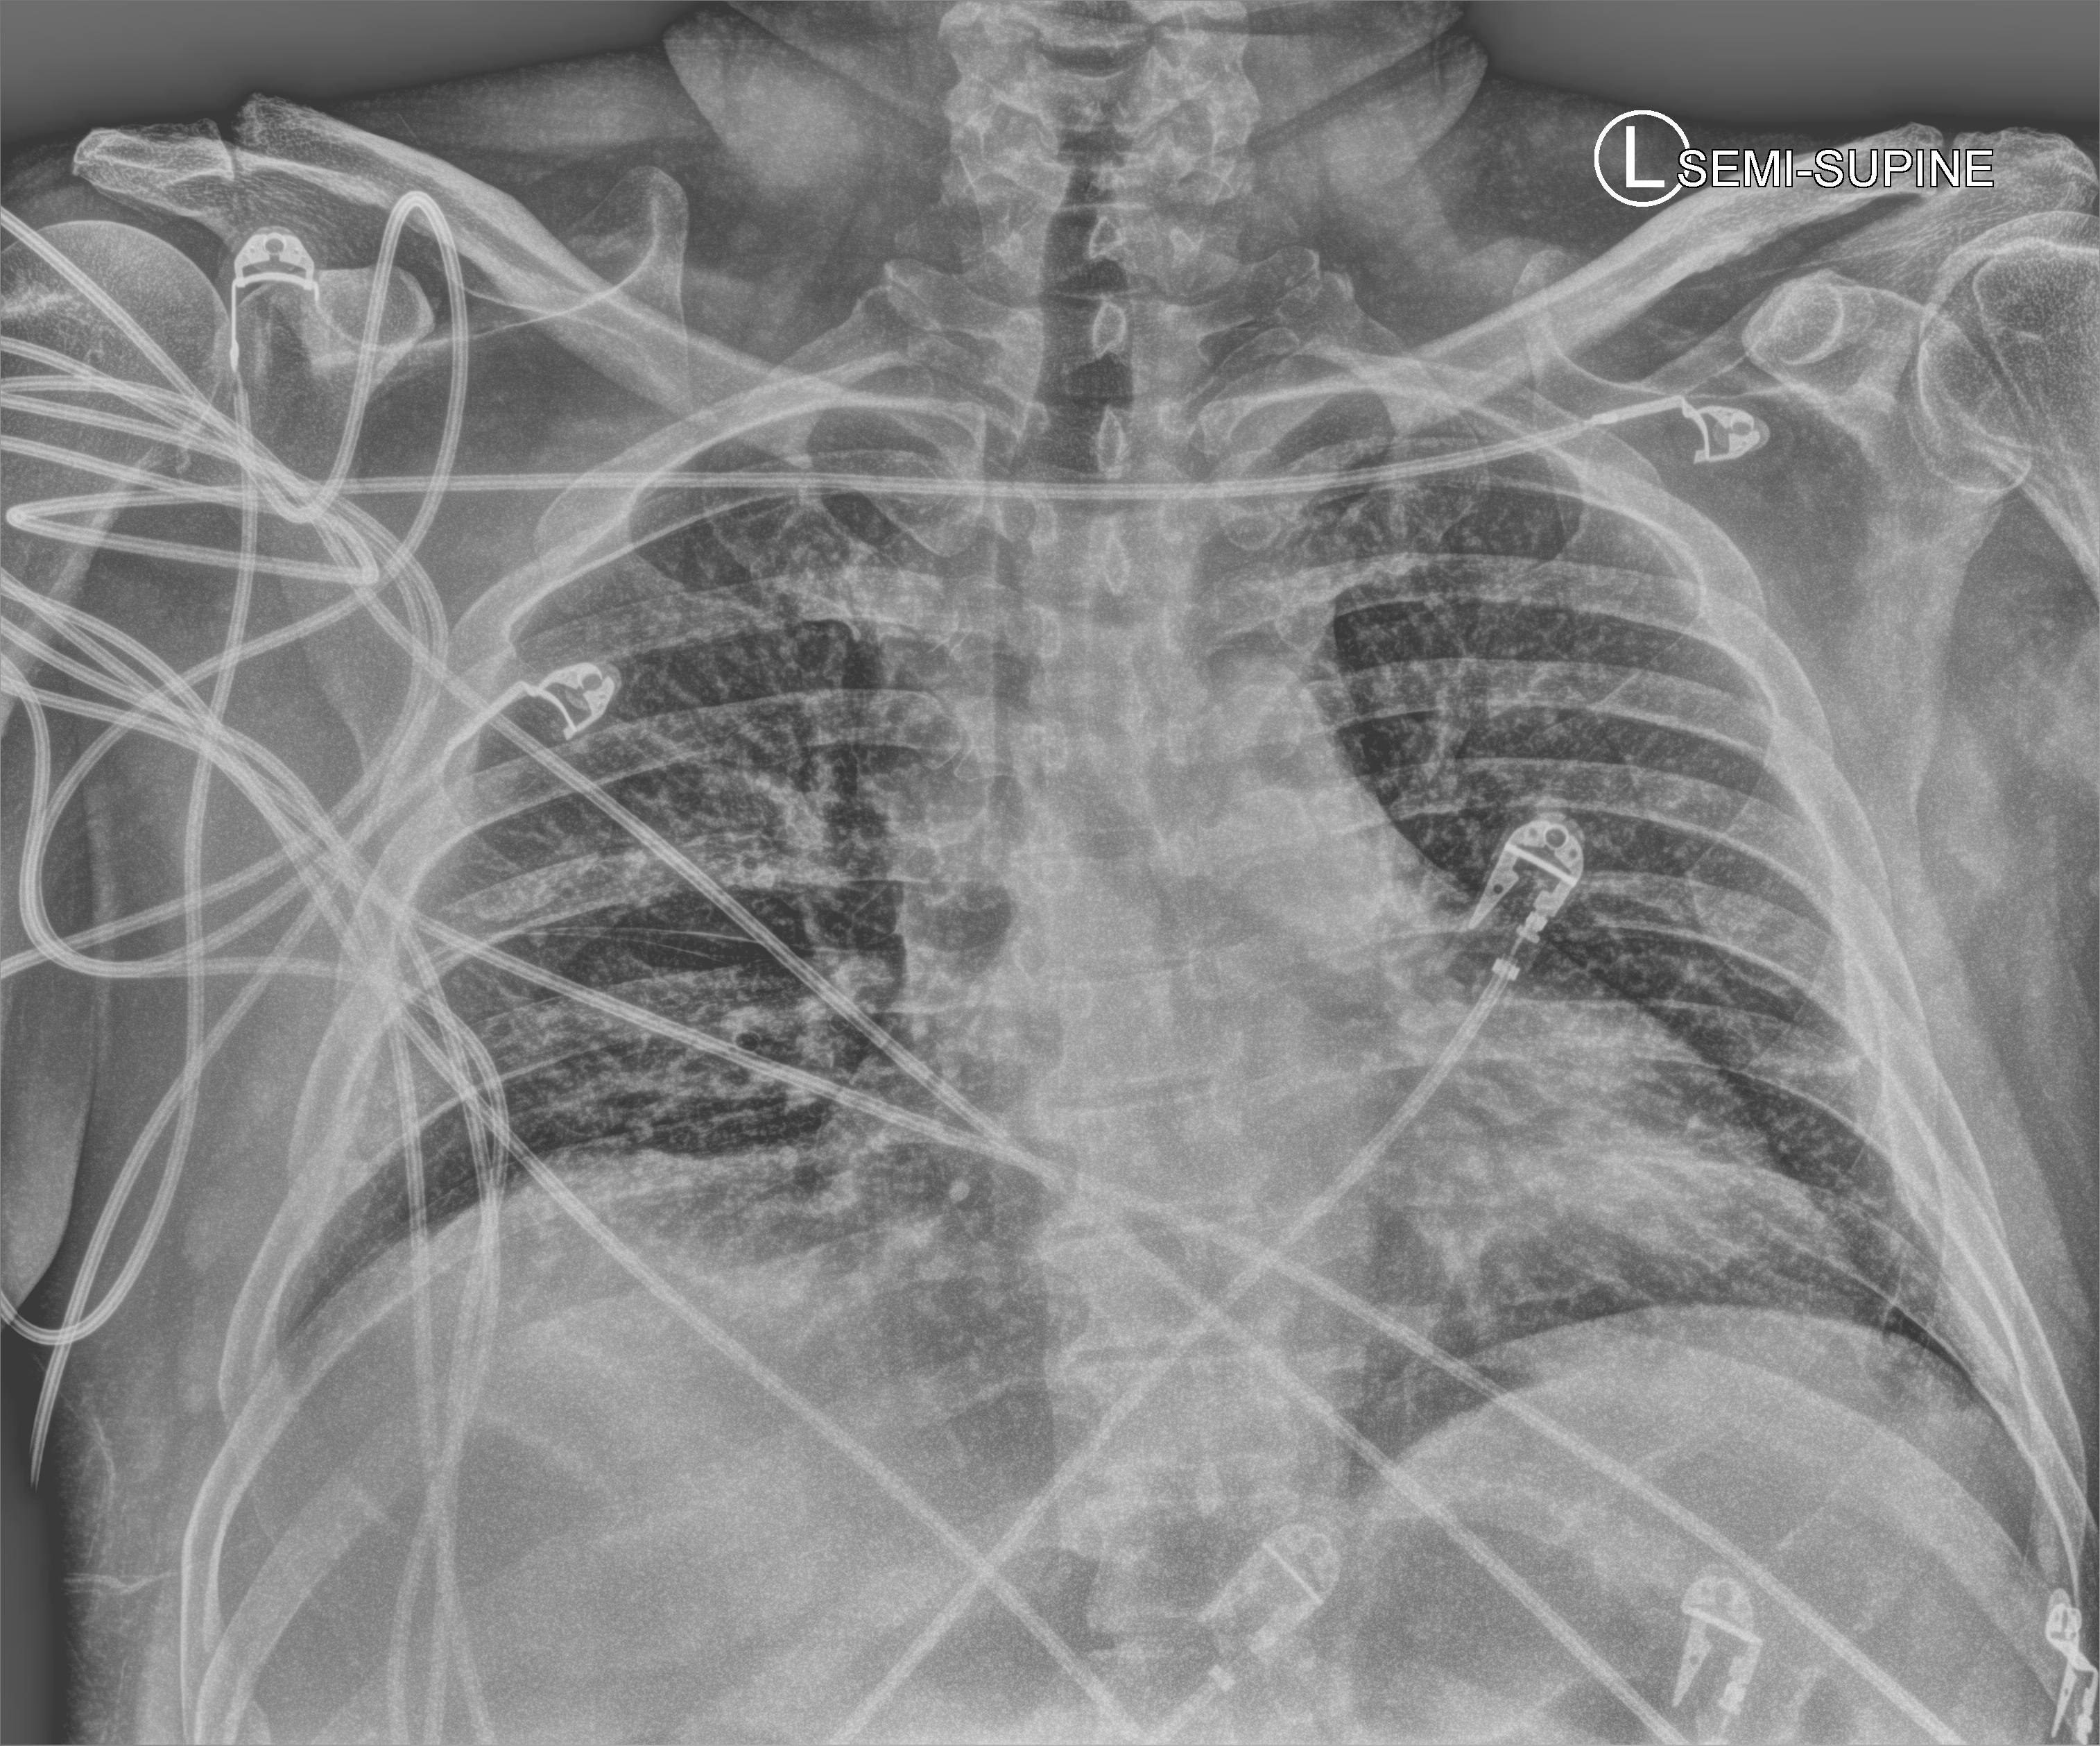
Bedside chest radiograph (computed radiography), anteroposterior (AP) projection. Male patient hospitalised with COVID-19, age 18–59 years.
Admission-level facts for this patient (not findings on this image; timing relative to this image not recorded): hypertension (admission record): yes; other chronic lung disease (admission record): no; admitted to intensive care during this hospital stay: yes.